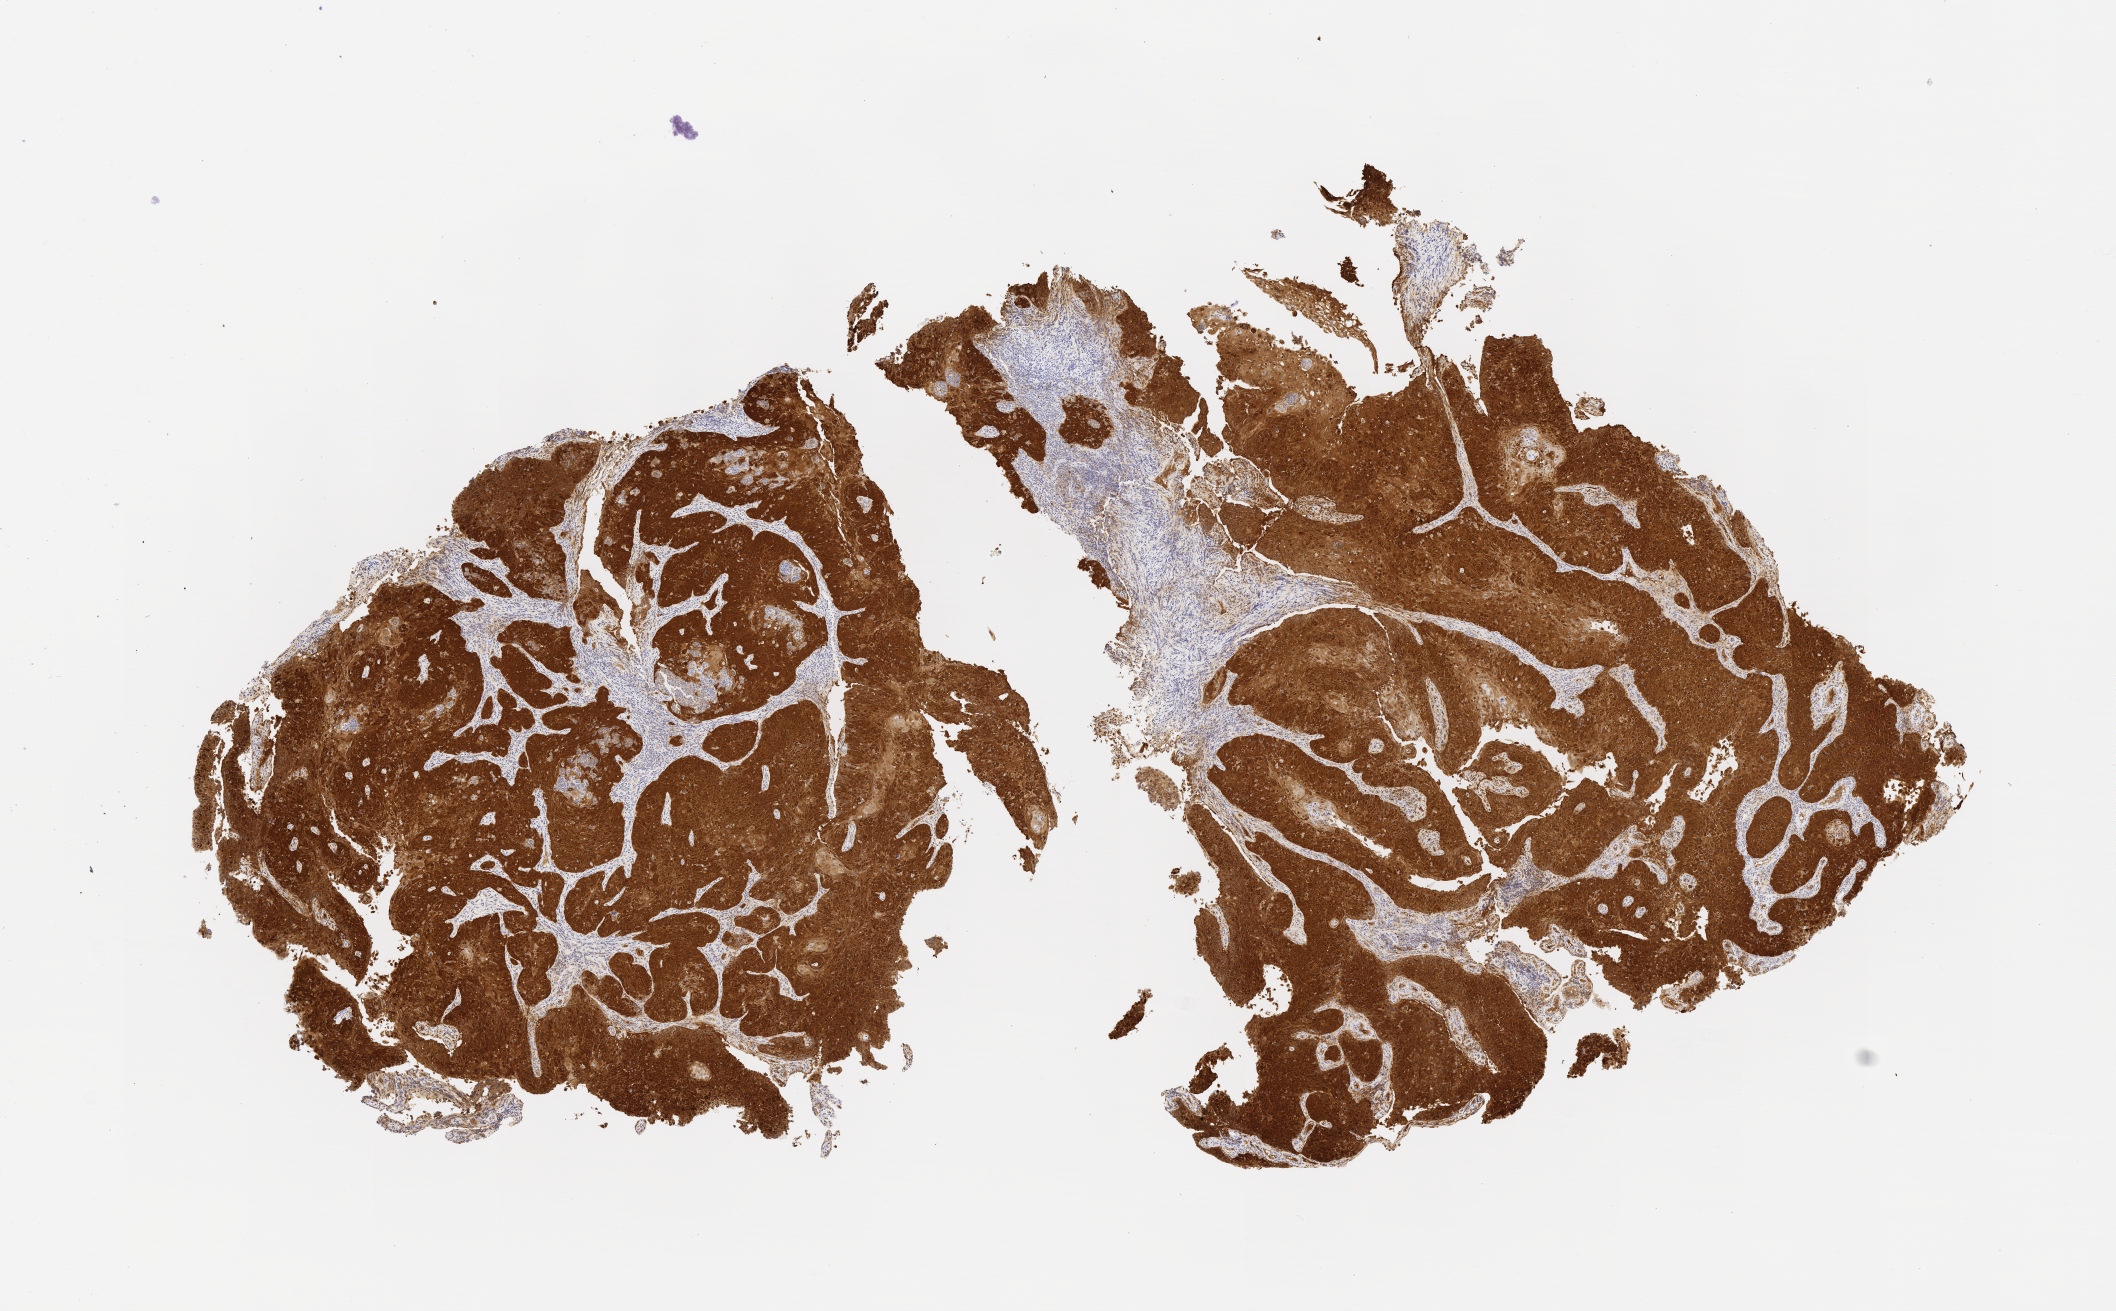
IHC for p16 (p16INK4a), whole-slide image — low-resolution overview of the scanned area, about 8.6 x 5.3 mm; specimen: tumor tissue; anatomic site: cervix. Patient female; age 33 years.
Diagnosis: Squamous cell carcinoma, large cell, nonkeratinizing, NOS.